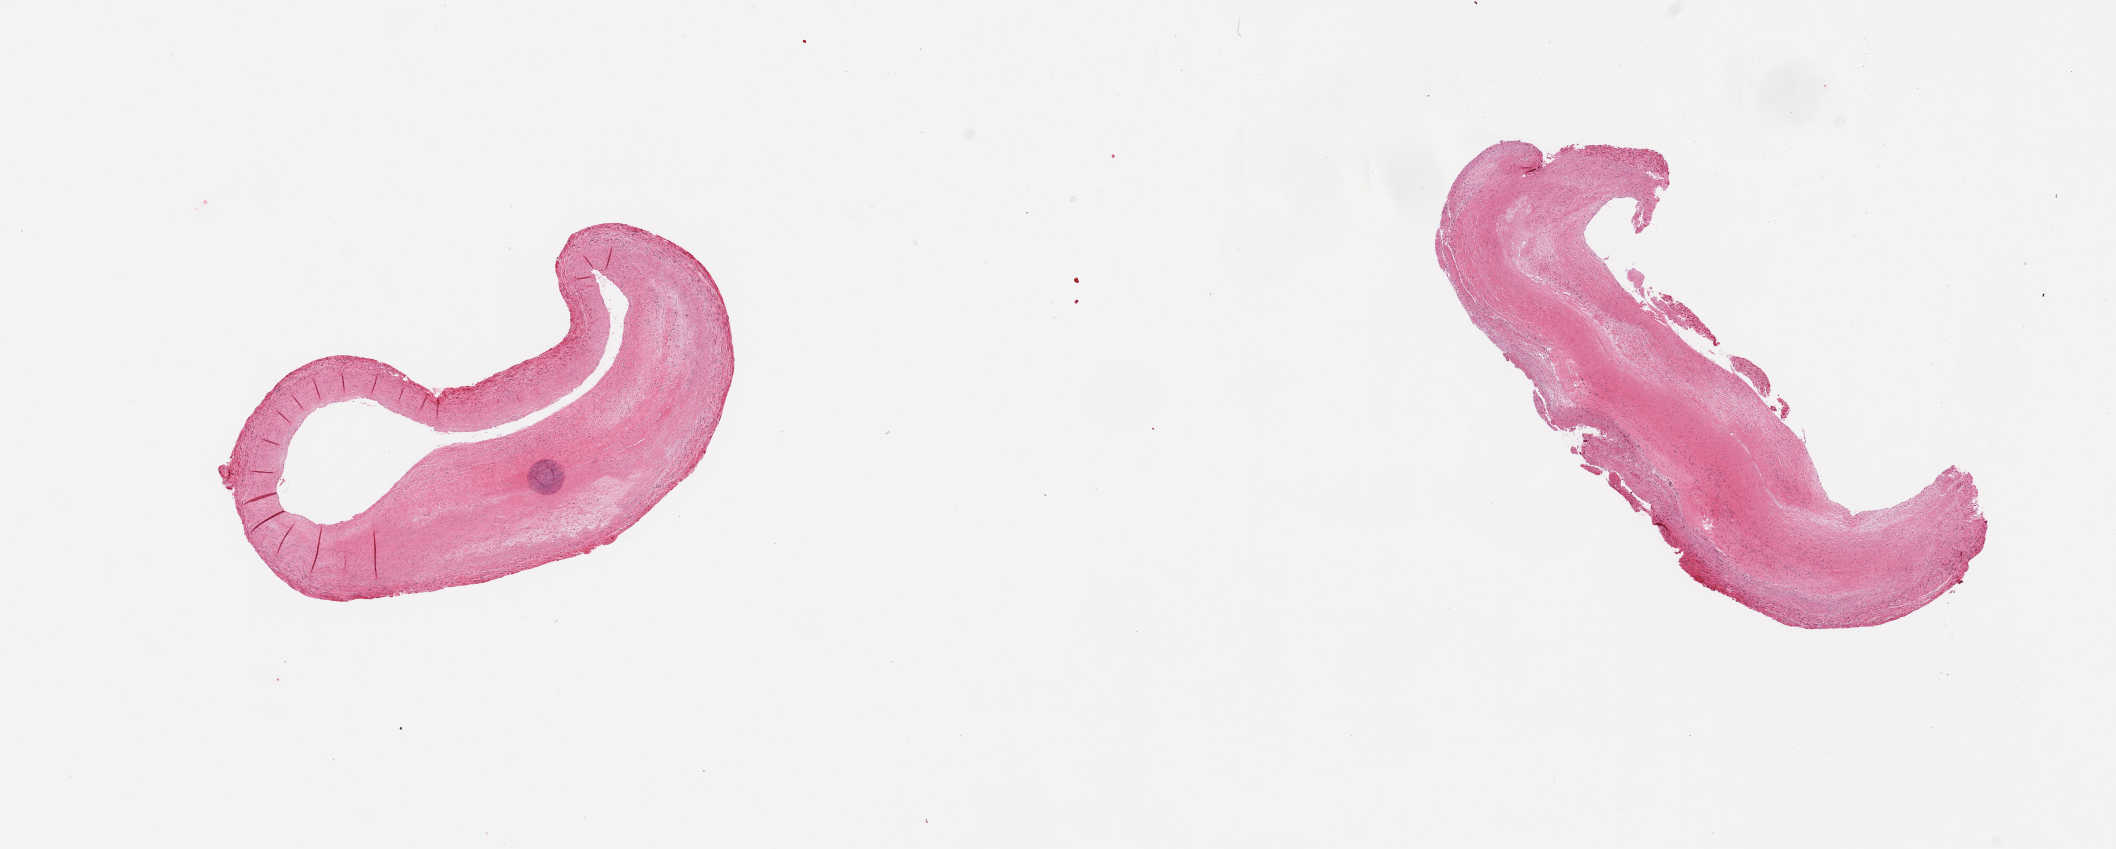
Whole-slide image, haematoxylin and eosin stain, brightfield, shown as a low-resolution overview of the whole scanned area (about 16.7 x 6.7 mm, slide scanned at 20x); PAXgene-fixed paraffin-embedded (PFPE) section; target tissue: coronary artery; tissue donor sample. Male donor.
Review note (as recorded): 2 pieces; eccentric fibrofatty plaques.